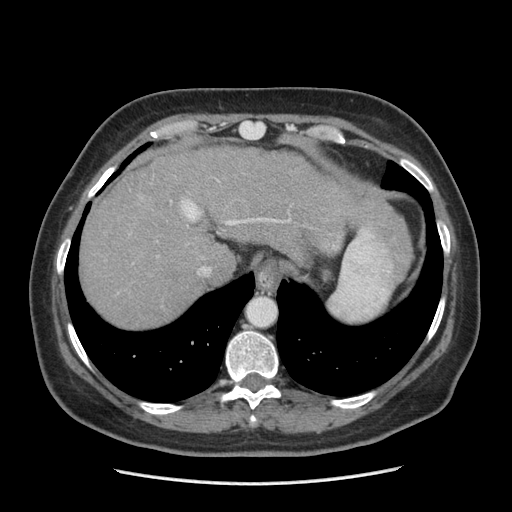
Contrast-enhanced abdominal CT (liver protocol), one axial slice. Position 166 of 185 along the scan axis. 140 kVp. Soft-tissue window (W 400 / L 40 HU). 2.5 mm slice thickness. 512 × 512 image matrix, field of view 360 × 360 mm. Case-level facts recorded for this patient, not image findings: diagnosis: hepatocellular carcinoma (patient treated with transarterial chemoembolisation; whether this scan precedes or follows treatment is not stated here); TNM stage (as recorded): Stage-I; Child-Pugh class: A; tumour differentiation: poorly differentiated; tumour nodularity: uninodular.
Outlined on this slice (semi-automatic segmentation, software-assisted and operator-edited):
- abdominal aorta: bounding box (x1, y1, x2, y2) in pixels: (247, 297, 275, 326)
- liver parenchyma outside the tumour (the mass and vessels are separate outlines, so this box may not span the whole liver): (80, 146, 394, 328)
- liver vessels: (182, 201, 276, 272)